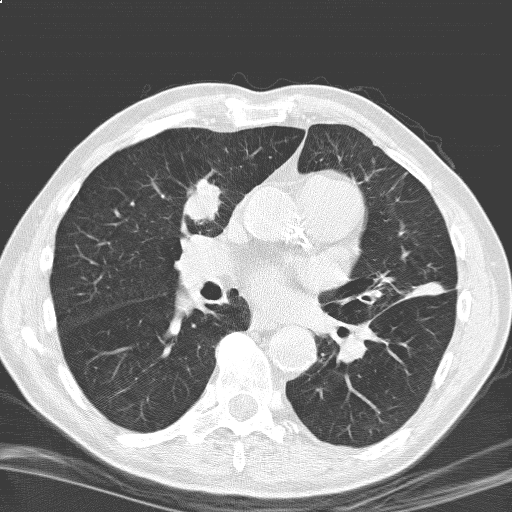
Low-dose screening chest CT, one axial slice. Slice 96 of 184 in the series (ordered by position). 120 kVp. Lung window (W 1500 / L -600 HU). 3.2 mm slice thickness. 512 × 512 image matrix, field of view 329 × 329 mm.
Annotated regions visible in this slice (outlined manually by an expert reader):
- lesion 1 (tumor, upper lobe of right lung): bounding box (x1, y1, x2, y2) in pixels: (184, 179, 220, 223)